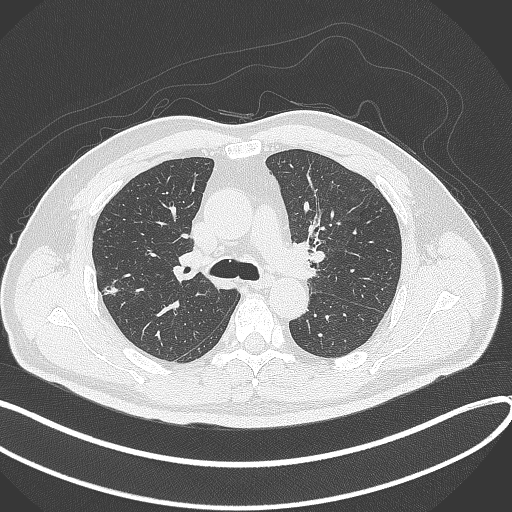
Chest CT, one axial slice; slice 223 of 372 in the series (ordered by position); 120 kVp; lung window (W 1500 / L -600 HU); 512 × 512 image matrix, field of view 400 × 400 mm. Patient: male, 60 years. Case-level facts recorded for this patient, not image findings: clinical TNM (as recorded): T1c N0 M0.
Outlined on this slice (bounding box drawn by a radiologist):
- lung tumour (recorded histology: adenocarcinoma): bounding box (x1, y1, x2, y2) in pixels: (99, 279, 123, 300)